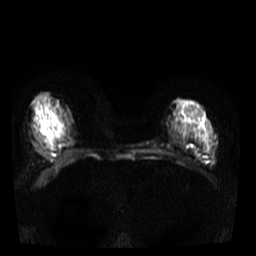
Breast MRI, one axial slice; position 17 of 40 along the scan axis; diffusion-weighted series; image 2 of 4 stored at this slice position (different b-values; order by instance number); 3 T; 5 mm slice thickness; 256 × 256 image matrix. Female patient.
Outlined on this slice (expert manual segmentation):
- tumour on diffusion-weighted imaging: box from (x=201, y=155) to (x=213, y=163) px